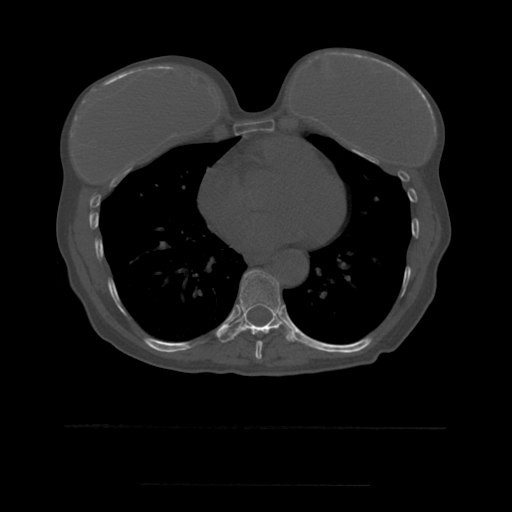
CT including the spine, one axial slice. Position 327 of 544 along the scan axis. Bone window (W 1800 / L 400 HU). 512 × 512 image matrix, field of view 350 × 350 mm. Patient age 58 years. Case-level facts recorded for this patient, not image findings: primary cancer: lung.
Outlined on this slice (semi-automatic segmentation, software-assisted and operator-edited):
- T8 vertebra: bounding box (x1, y1, x2, y2) in pixels: (247, 329, 270, 360)
- T9 vertebra: (216, 270, 299, 343)